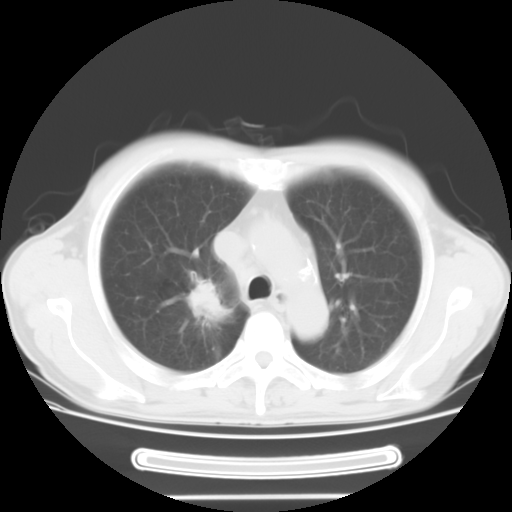
Chest CT, one axial slice. Position 17 of 24 along the scan axis. 120 kVp. Lung window (W 1500 / L -600 HU). 10 mm slice thickness. 512 × 512 image matrix. Male patient, age 57 years. Case-level facts recorded for this patient, not image findings: clinical TNM (as recorded): T2 N3 M1b.
Structures marked on this image (rectangle marked by the reading radiologist):
- lung tumour (recorded histology: adenocarcinoma): bounding box [x1, y1, x2, y2] px = [181, 278, 228, 324]